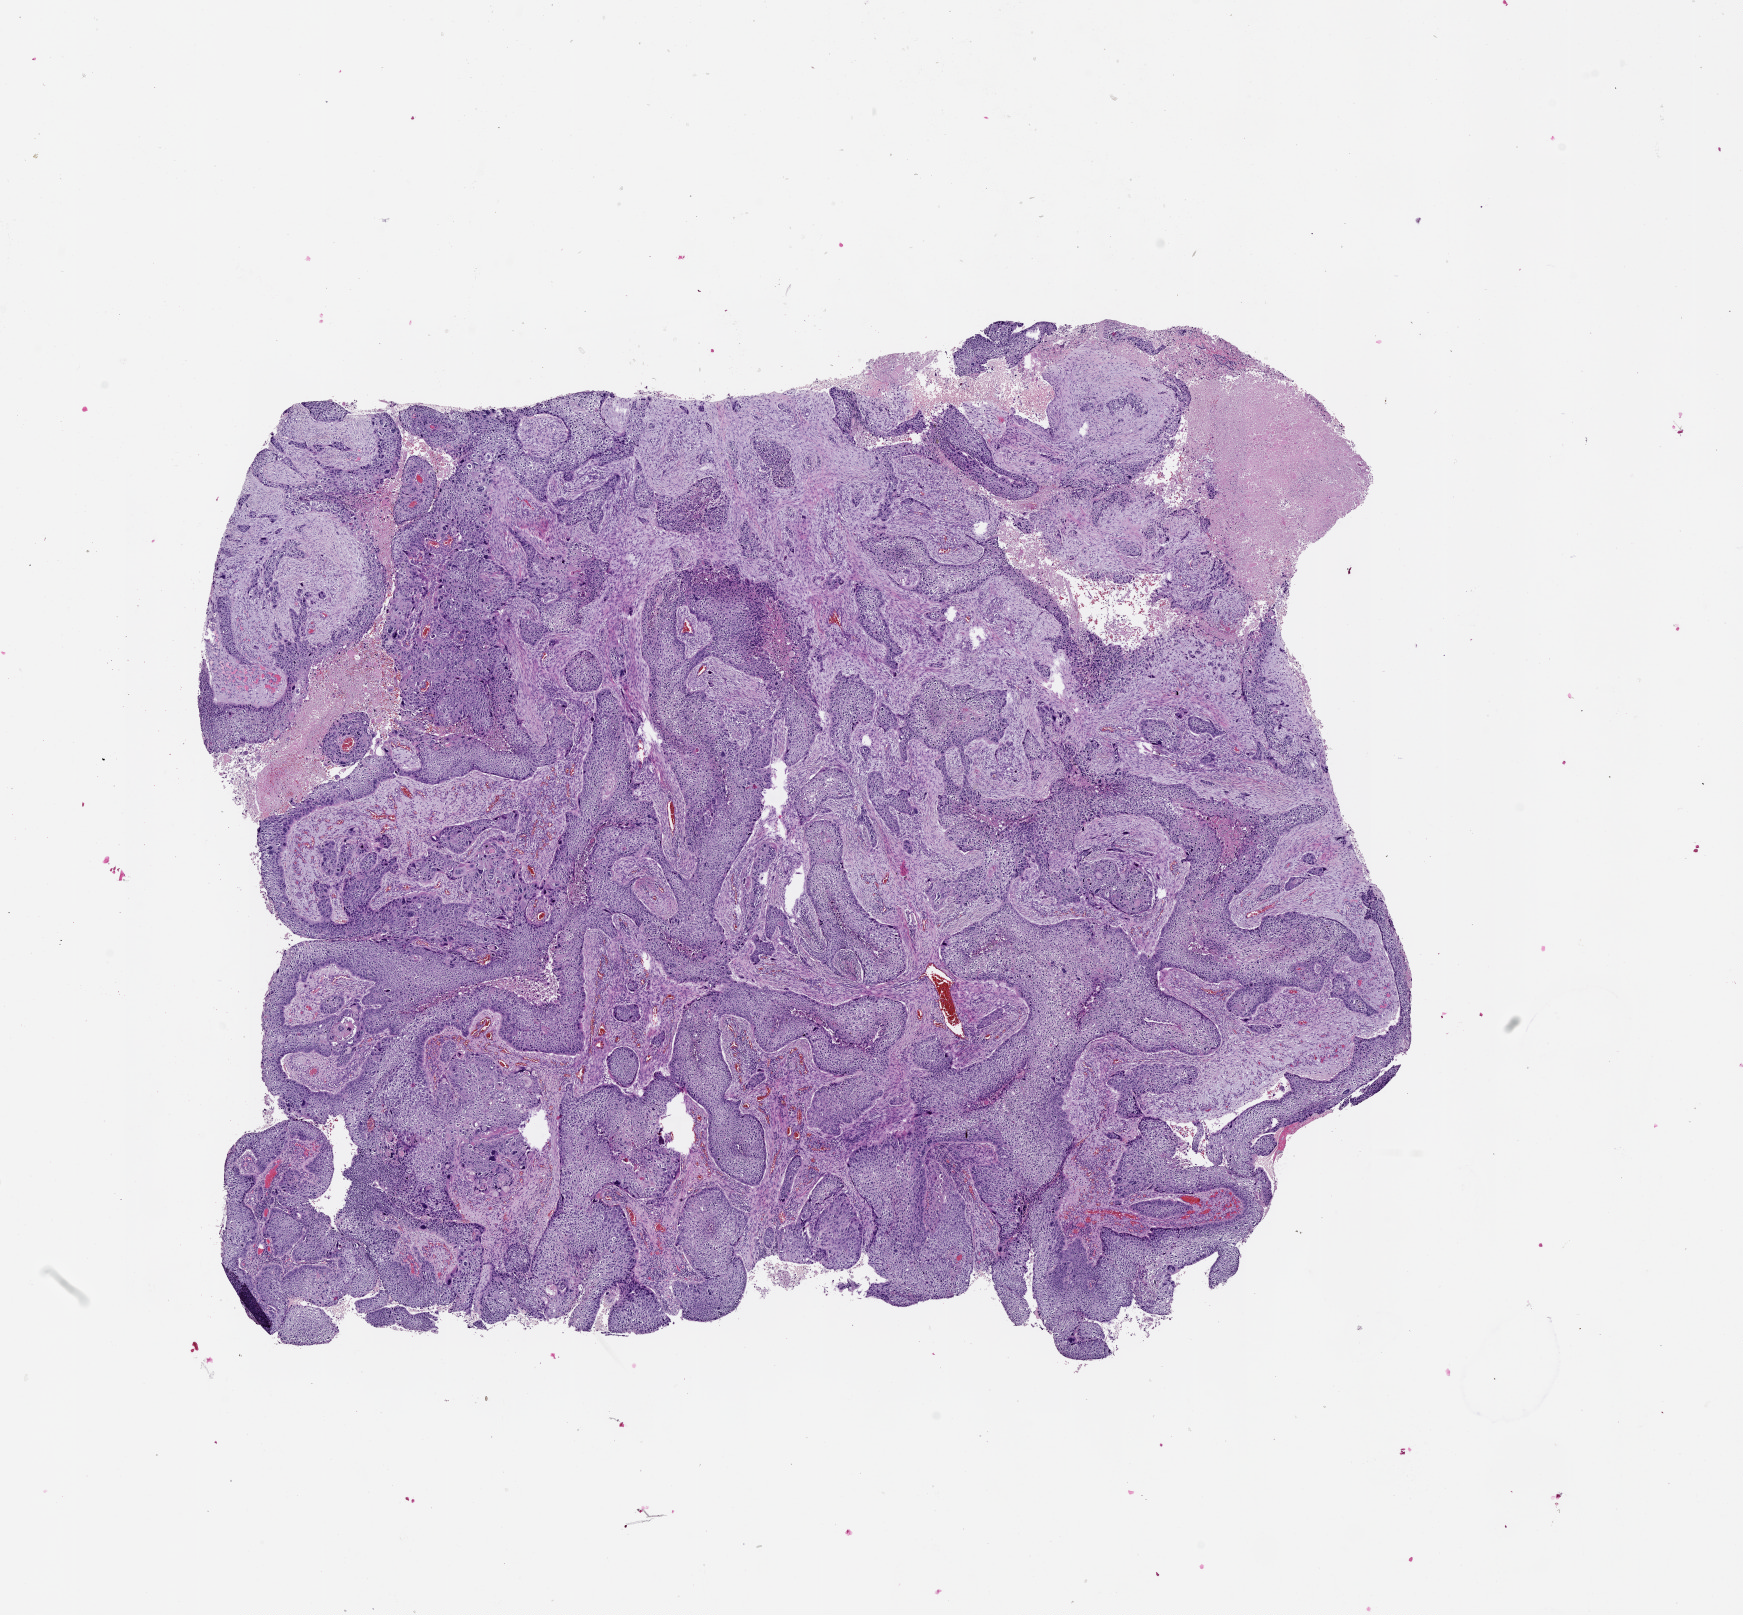
Whole-slide histology image, Hematoxylin and eosin (H&E) stained, shown as a low-resolution overview of the whole scanned area (about 14.0 x 13.0 mm, acquisition: 20x scan), lung, tumour tissue. Male, 55 y/o.
Patient diagnosis (cohort enrolment): squamous cell carcinoma (lung).